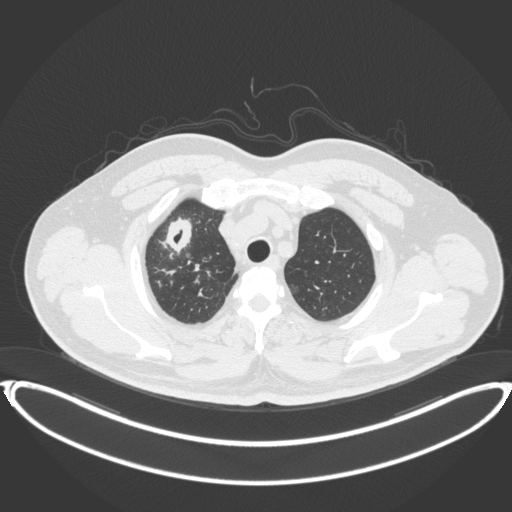
Chest CT, one axial slice. Position 326 of 399 along the scan axis. Reconstruction kernel B31f. 120 kVp. Lung window (W 1500 / L -600 HU). 1 mm slice thickness. 512 × 512 image matrix, field of view 445 × 445 mm. Patient: male, 53 years. Case-level facts recorded for this patient, not image findings: clinical TNM (as recorded): T2a N0 M0.
Structures marked on this image (rectangle marked by the reading radiologist):
- lung tumour (recorded histology: adenocarcinoma): bounding box <162,214,201,259> (left, top, right, bottom; pixels)